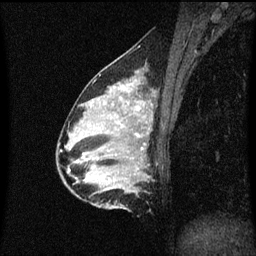
Breast MRI (dynamic contrast-enhanced), one sagittal slice; slice 23 of 60 in the series (ordered by position); dynamic contrast-enhanced series, image 2 of 3 at this slice position (ordered by acquisition); 1.5 T; TE 4.2 ms, TR 8.4 ms; 2 mm slice thickness; 256 × 256 image matrix, field of view 200 × 200 mm. Patient: female, 34 years. From the clinical record (not read from this slice): setting: breast cancer imaged before/during neoadjuvant chemotherapy; receptor status: HR-positive, HER2-negative.
Annotated regions visible in this slice (semi-automatic segmentation, software-assisted and operator-edited):
- analysis volume of interest (the breast-tissue region the enhancement analysis was run in; not a lesion): bounding box <69,70,154,209> (left, top, right, bottom; pixels)
- tumour enhancement mask (voxels above the 70 % enhancement threshold inside the analysis volume of interest): <136,106,140,111>